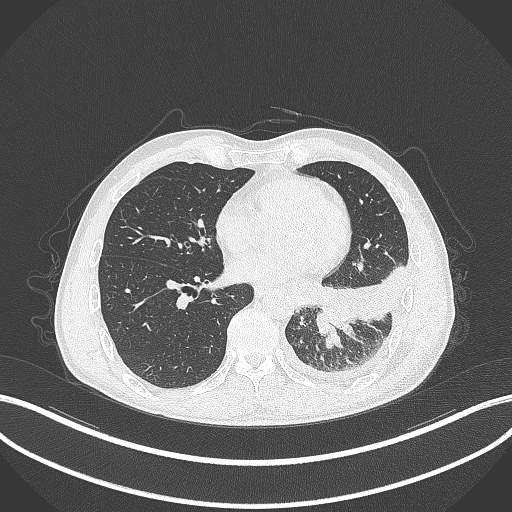
Chest CT, one axial slice; slice 121 of 295 in the series (ordered by position); 120 kVp; lung window (W 1500 / L -600 HU); 1 mm slice thickness; 512 × 512 image matrix. Patient: male, 47 years. From the clinical record (not read from this slice): clinical TNM (as recorded): T3 N1 M1c.
Outlined on this slice (bounding box drawn by a radiologist):
- lung tumour (recorded histology: small cell carcinoma): bounding box [x1, y1, x2, y2] px = [315, 297, 358, 338]